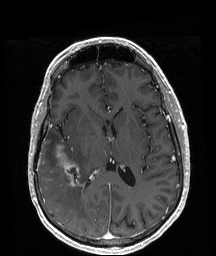
Brain MRI from a brain-tumour surgery series, one axial slice. Slice 97 of 208 in the series (ordered by position). T1-weighted post-contrast. 1 mm slice thickness. 216 × 256 image matrix, field of view 211 × 250 mm. Case-level facts recorded for this patient, not image findings: histopathology: Astrocytoma; WHO grade: 4; IDH mutation: yes.
Structures marked on this image (manually delineated by an expert):
- tumour: bounding box [x1, y1, x2, y2] px = [56, 145, 80, 187]